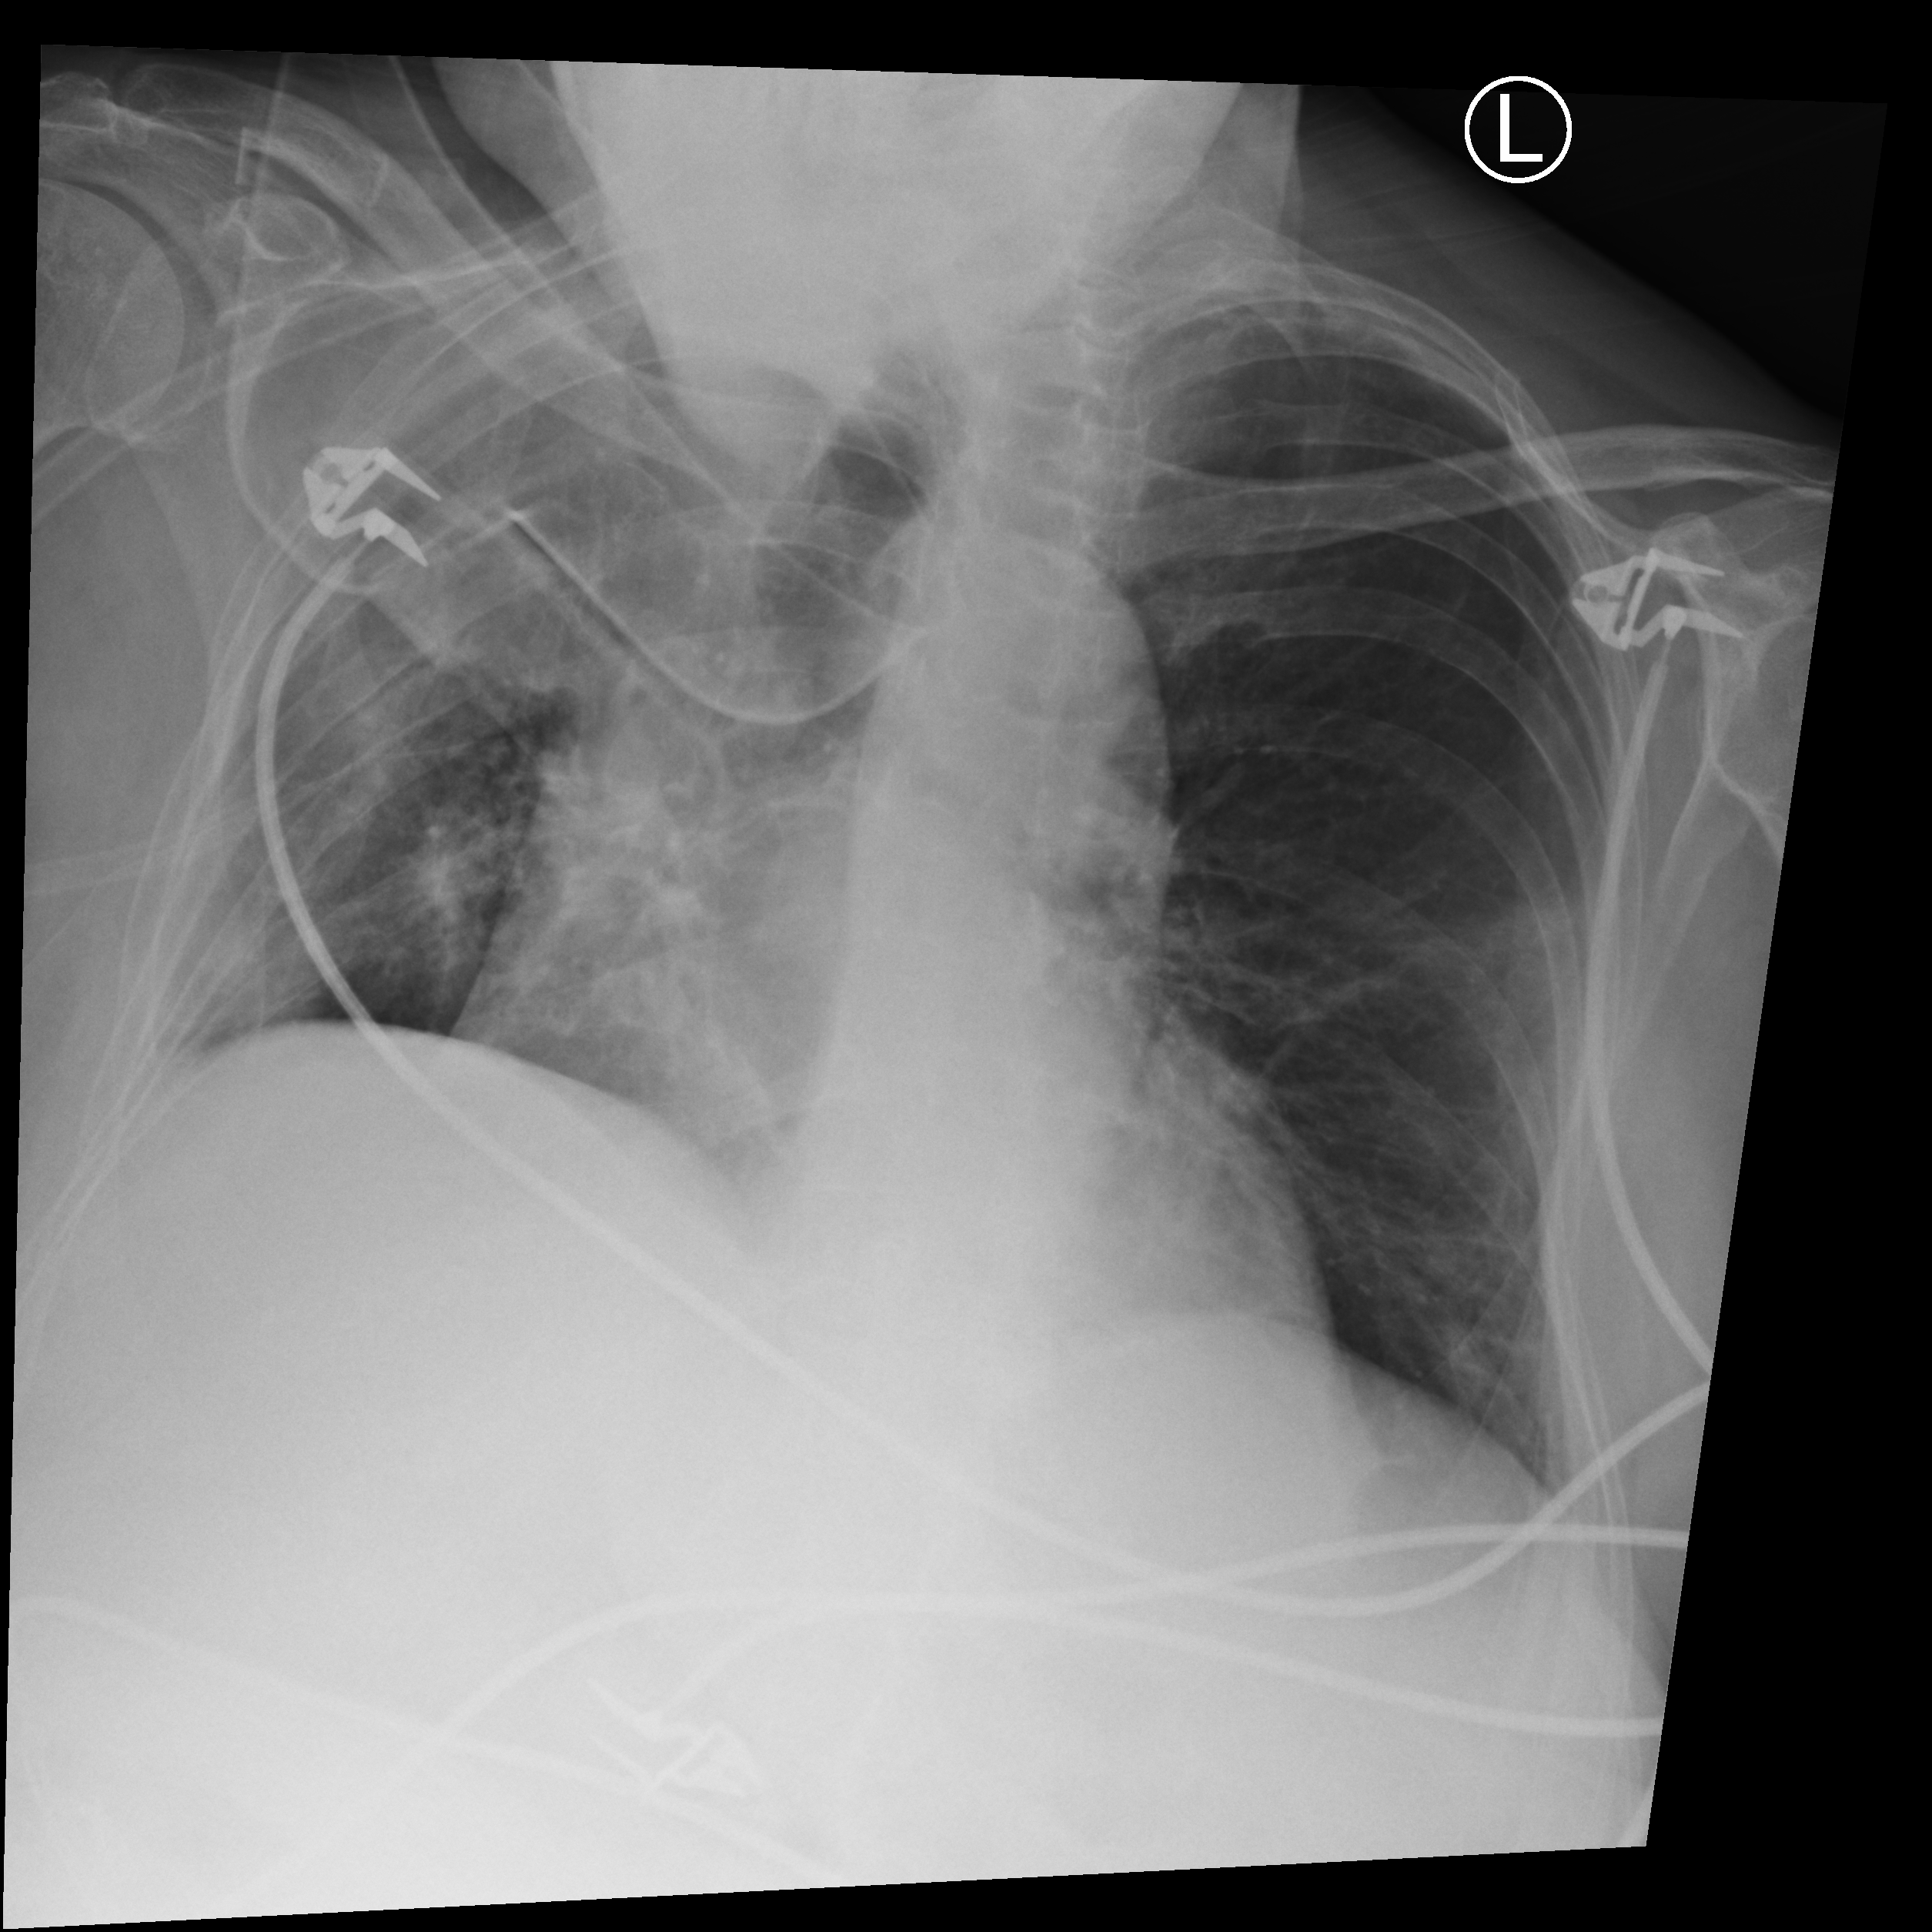
Bedside chest radiograph (computed radiography); anteroposterior (AP) projection. Patient hospitalised with COVID-19; female, aged 75–90 years.
From the hospital-stay record, not from the radiograph (when in the stay this image was taken is not recorded): admitted to intensive care during this hospital stay: yes; mechanically ventilated during this hospital stay: yes.